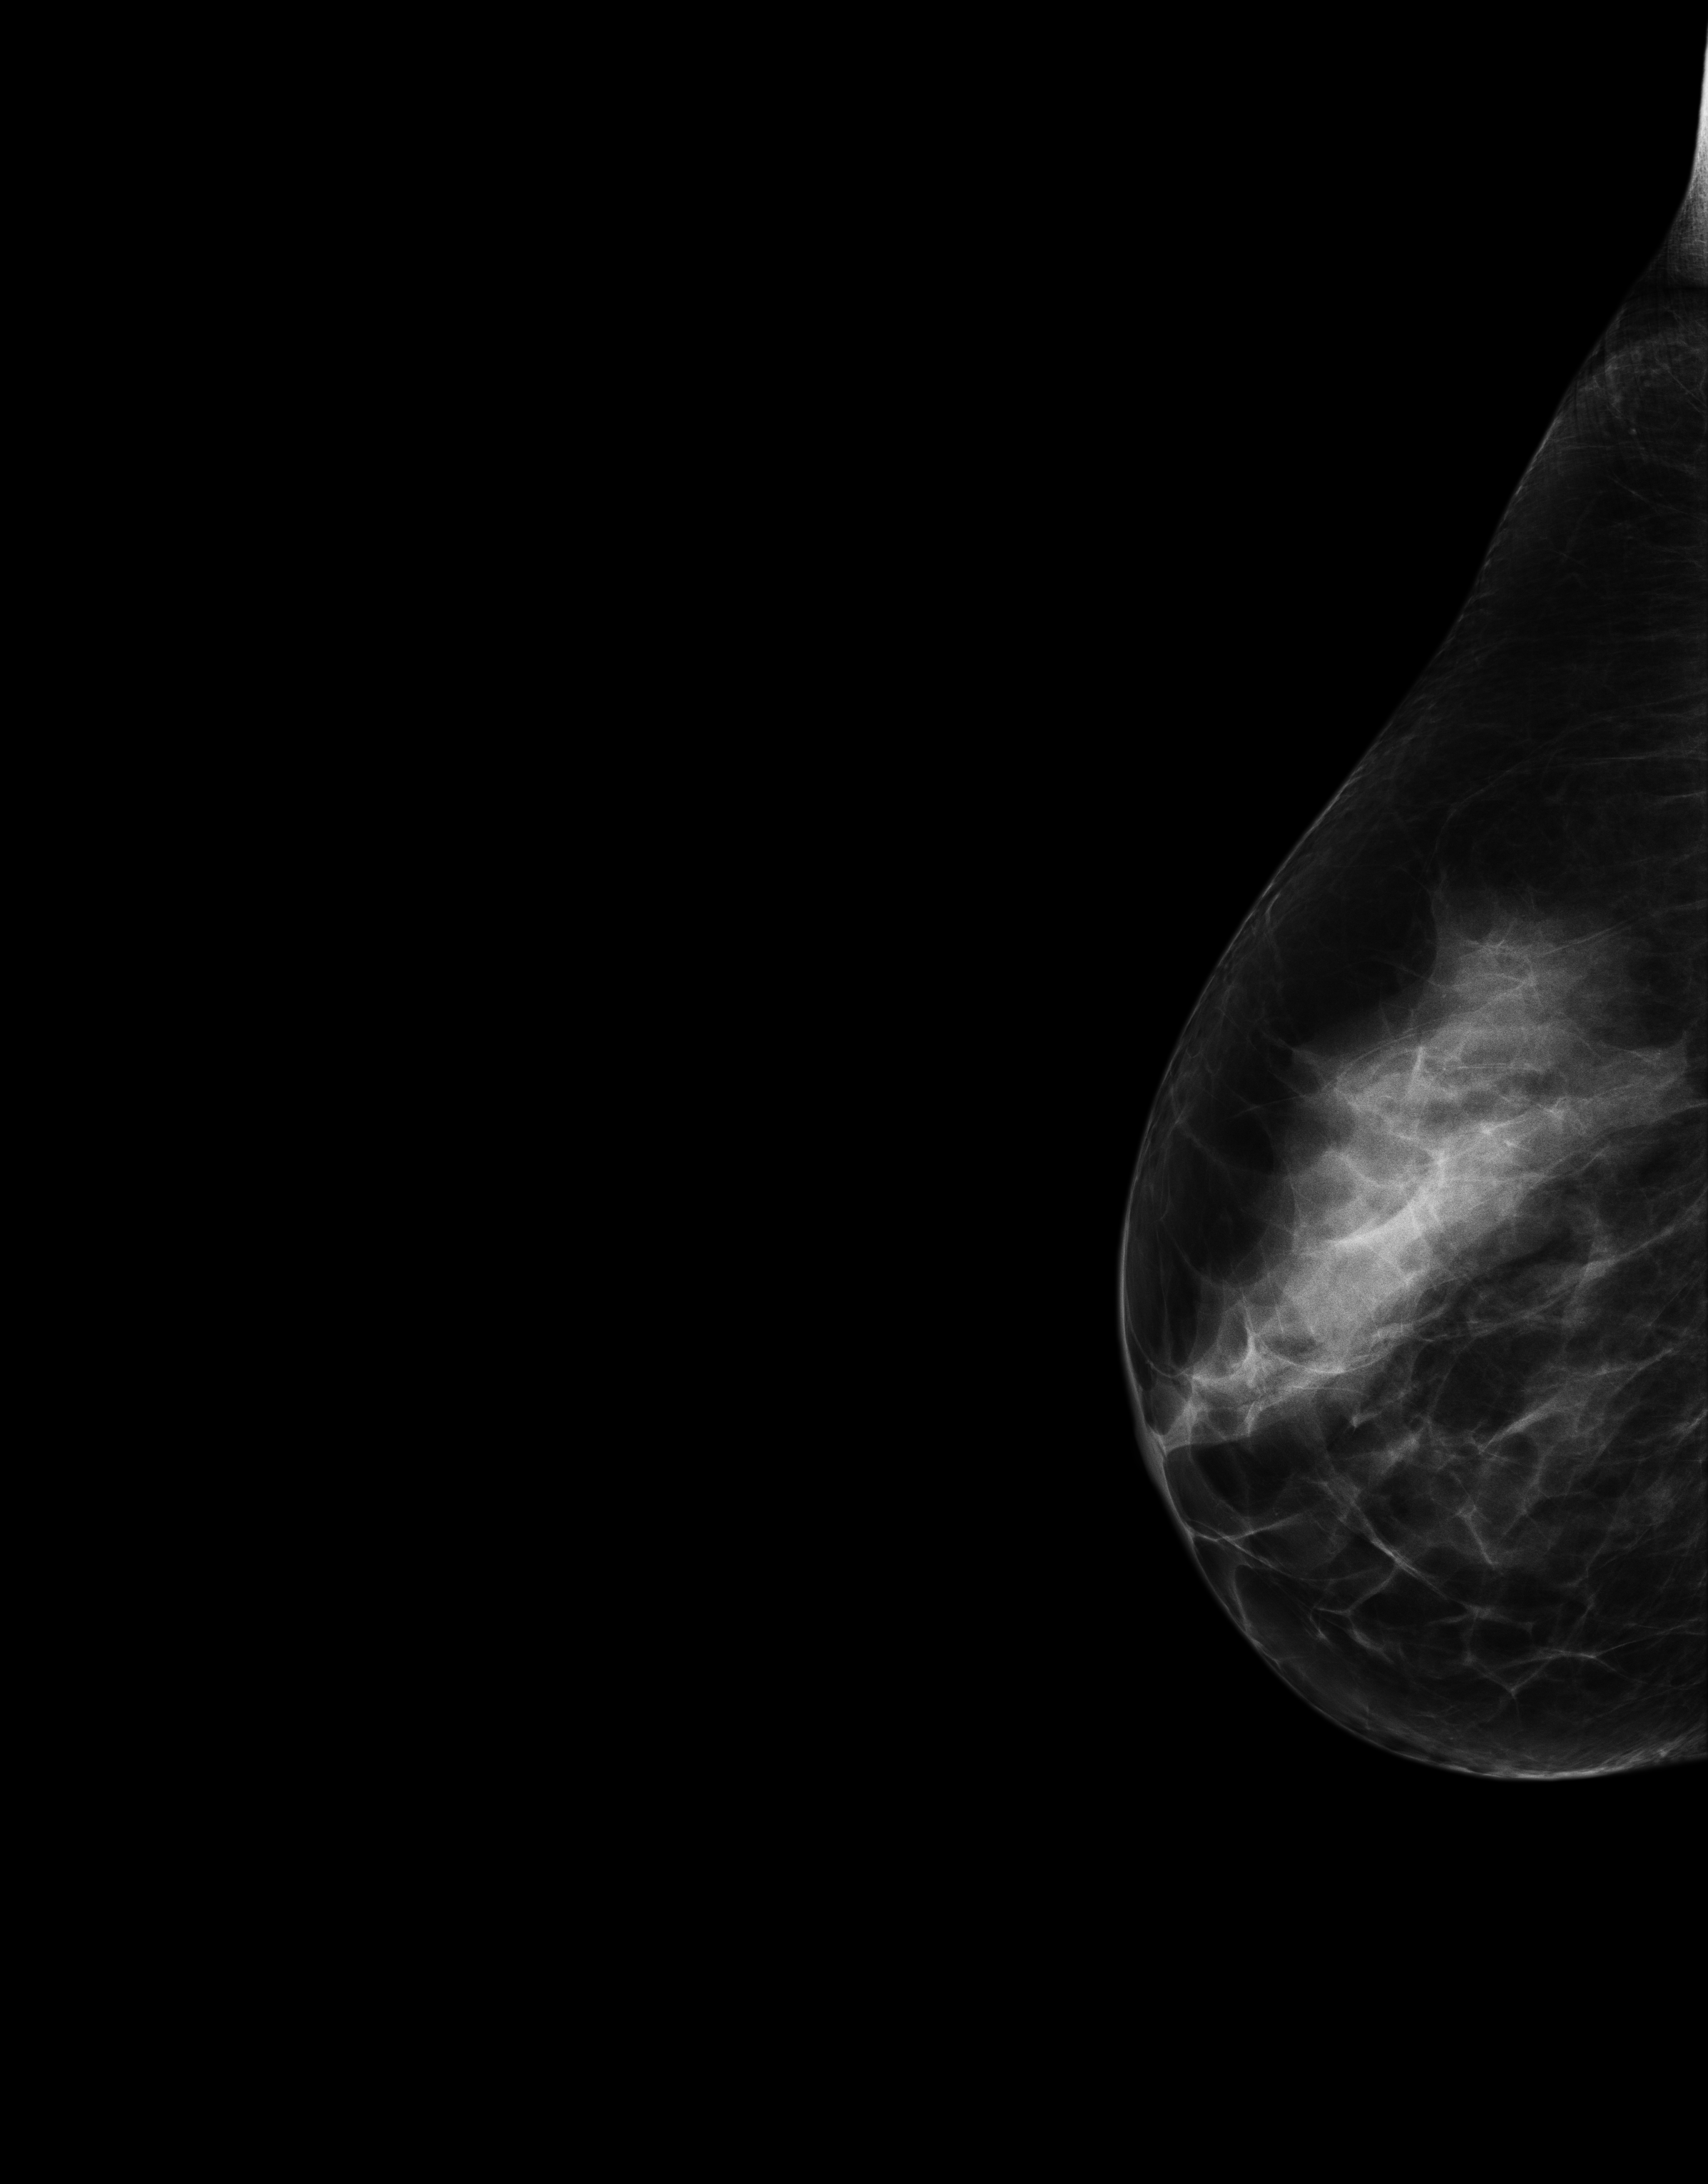
Full-field digital mammogram (FFDM); right breast; laterally exaggerated craniocaudal (XCCL) view; screening examination; system: Senographe Essential ADS_56.21.3. Patient: female, 51 years.
- breast density at the screening exam (both breasts): heterogeneously dense (BI-RADS density category c)
- final BI-RADS category for the screening round (tomosynthesis exam, both breasts): category 1
- recall: no recall after this screen